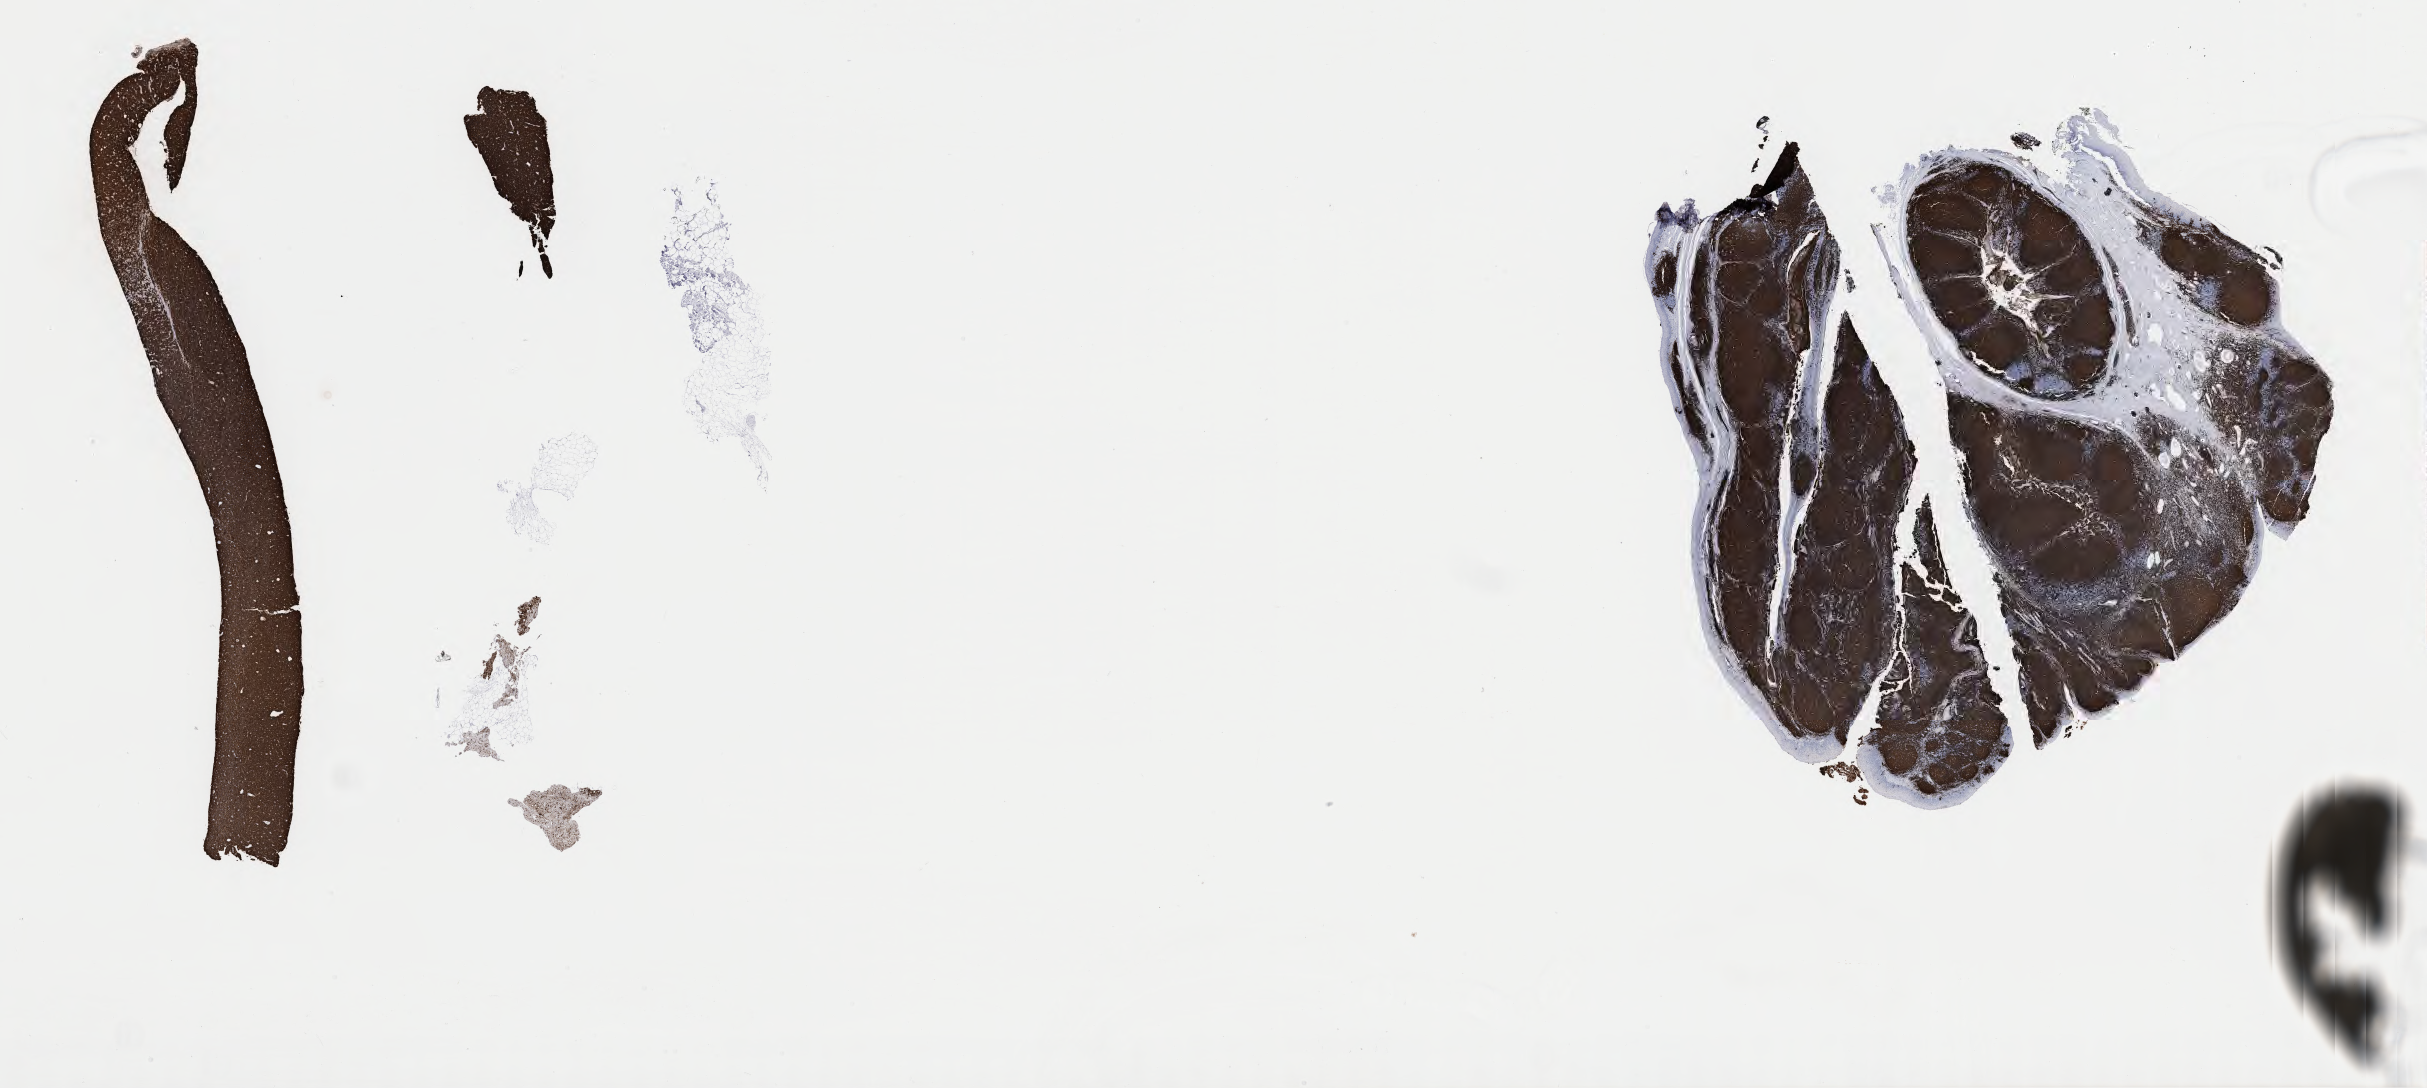
Whole-slide image, immunohistochemical stain for CD20 — a low-resolution overview of the entire scanned area, about 39.3 x 17.6 mm, specimen: tumor tissue. Patient female; 61 years old.
Histologic diagnosis: Burkitt lymphoma, NOS.